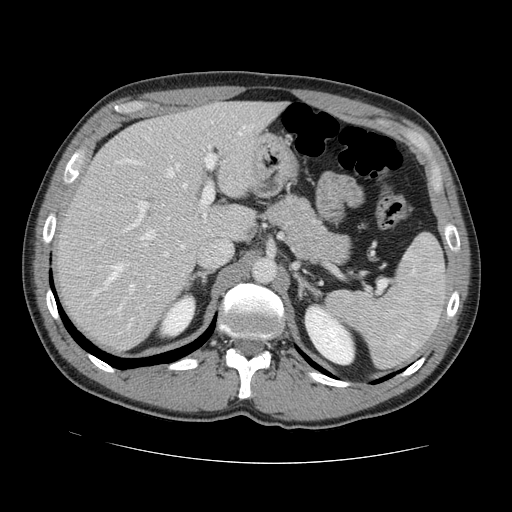
Contrast-enhanced abdominal CT, one axial slice. Position 89 of 131 along the scan axis. Intravenous contrast given. Soft-tissue window (W 400 / L 40 HU). 2.5 mm slice thickness. 512 × 512 image matrix. Male patient, age 40 years. From the clinical record (not read from this slice): diagnosis: colorectal cancer liver metastases, imaged before liver resection; multiple liver metastases: yes; largest metastasis: 2.9 cm.
Outlined on this slice (manually delineated by an expert):
- hepatic veins: bounding box <93,158,187,320> (left, top, right, bottom; pixels)
- liver: <60,103,280,349>
- planned liver remnant (the part of the liver to remain after resection): <101,103,281,239>
- portal vein (with intrahepatic branches): <98,154,215,314>